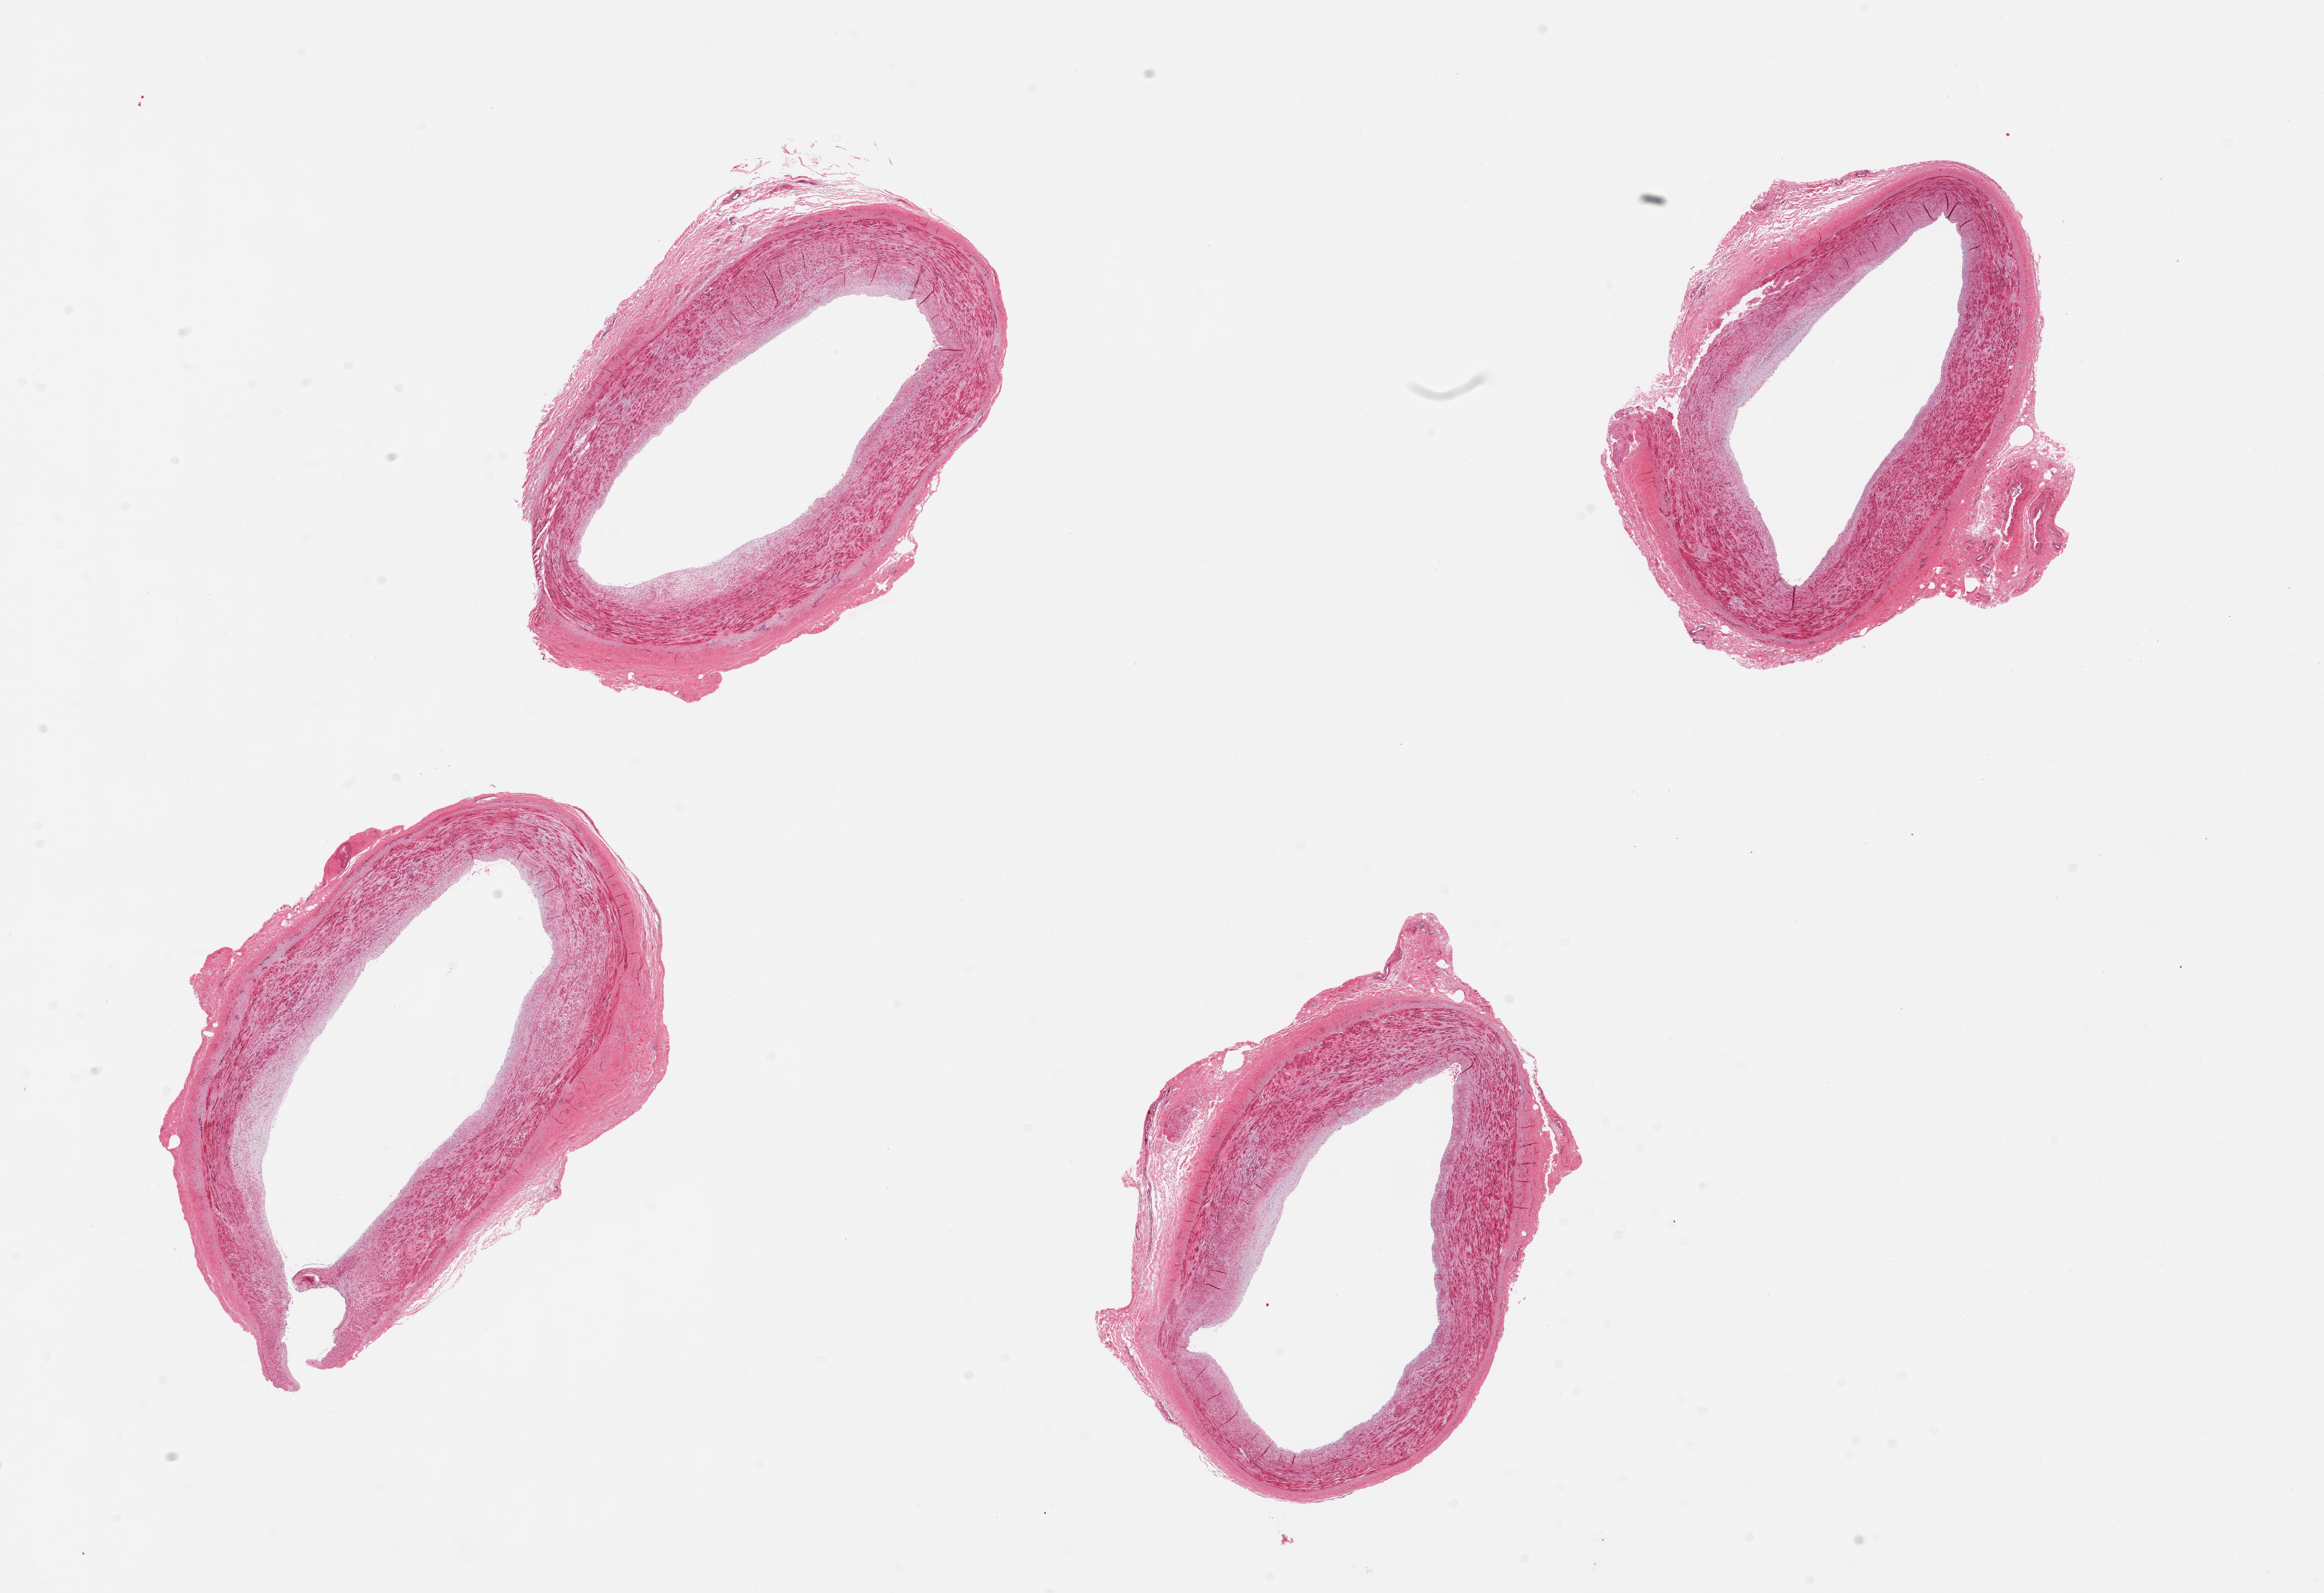
Digitized haematoxylin and eosin-stained section — shown as a low-resolution overview of the whole scanned area (about 25.6 x 17.5 mm), PAXgene-fixed paraffin-embedded (PFPE) section, section of tibial artery (target tissue), donor tissue sample. Donor: female.
Pathologist's review note for this sample: 4 pieces, intimal thickening/early atherosclerotic change.